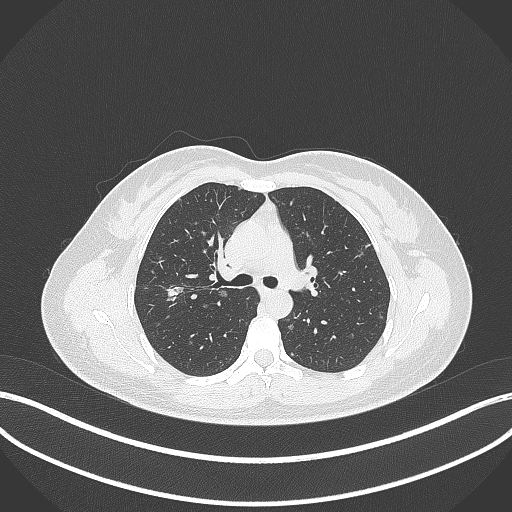
Chest CT, one axial slice. Slice 219 of 307 in the series (ordered by position). Lung window (W 1500 / L -600 HU). 512 × 512 image matrix, field of view 400 × 400 mm. Patient: female, 33 years. From the clinical record (not read from this slice): clinical TNM (as recorded): T1c N0 M0; histopathological grade: G2-G3.
Outlined on this slice (bounding box drawn by a radiologist):
- lung tumour (recorded histology: adenocarcinoma): bounding box [x1, y1, x2, y2] px = [165, 282, 187, 300]